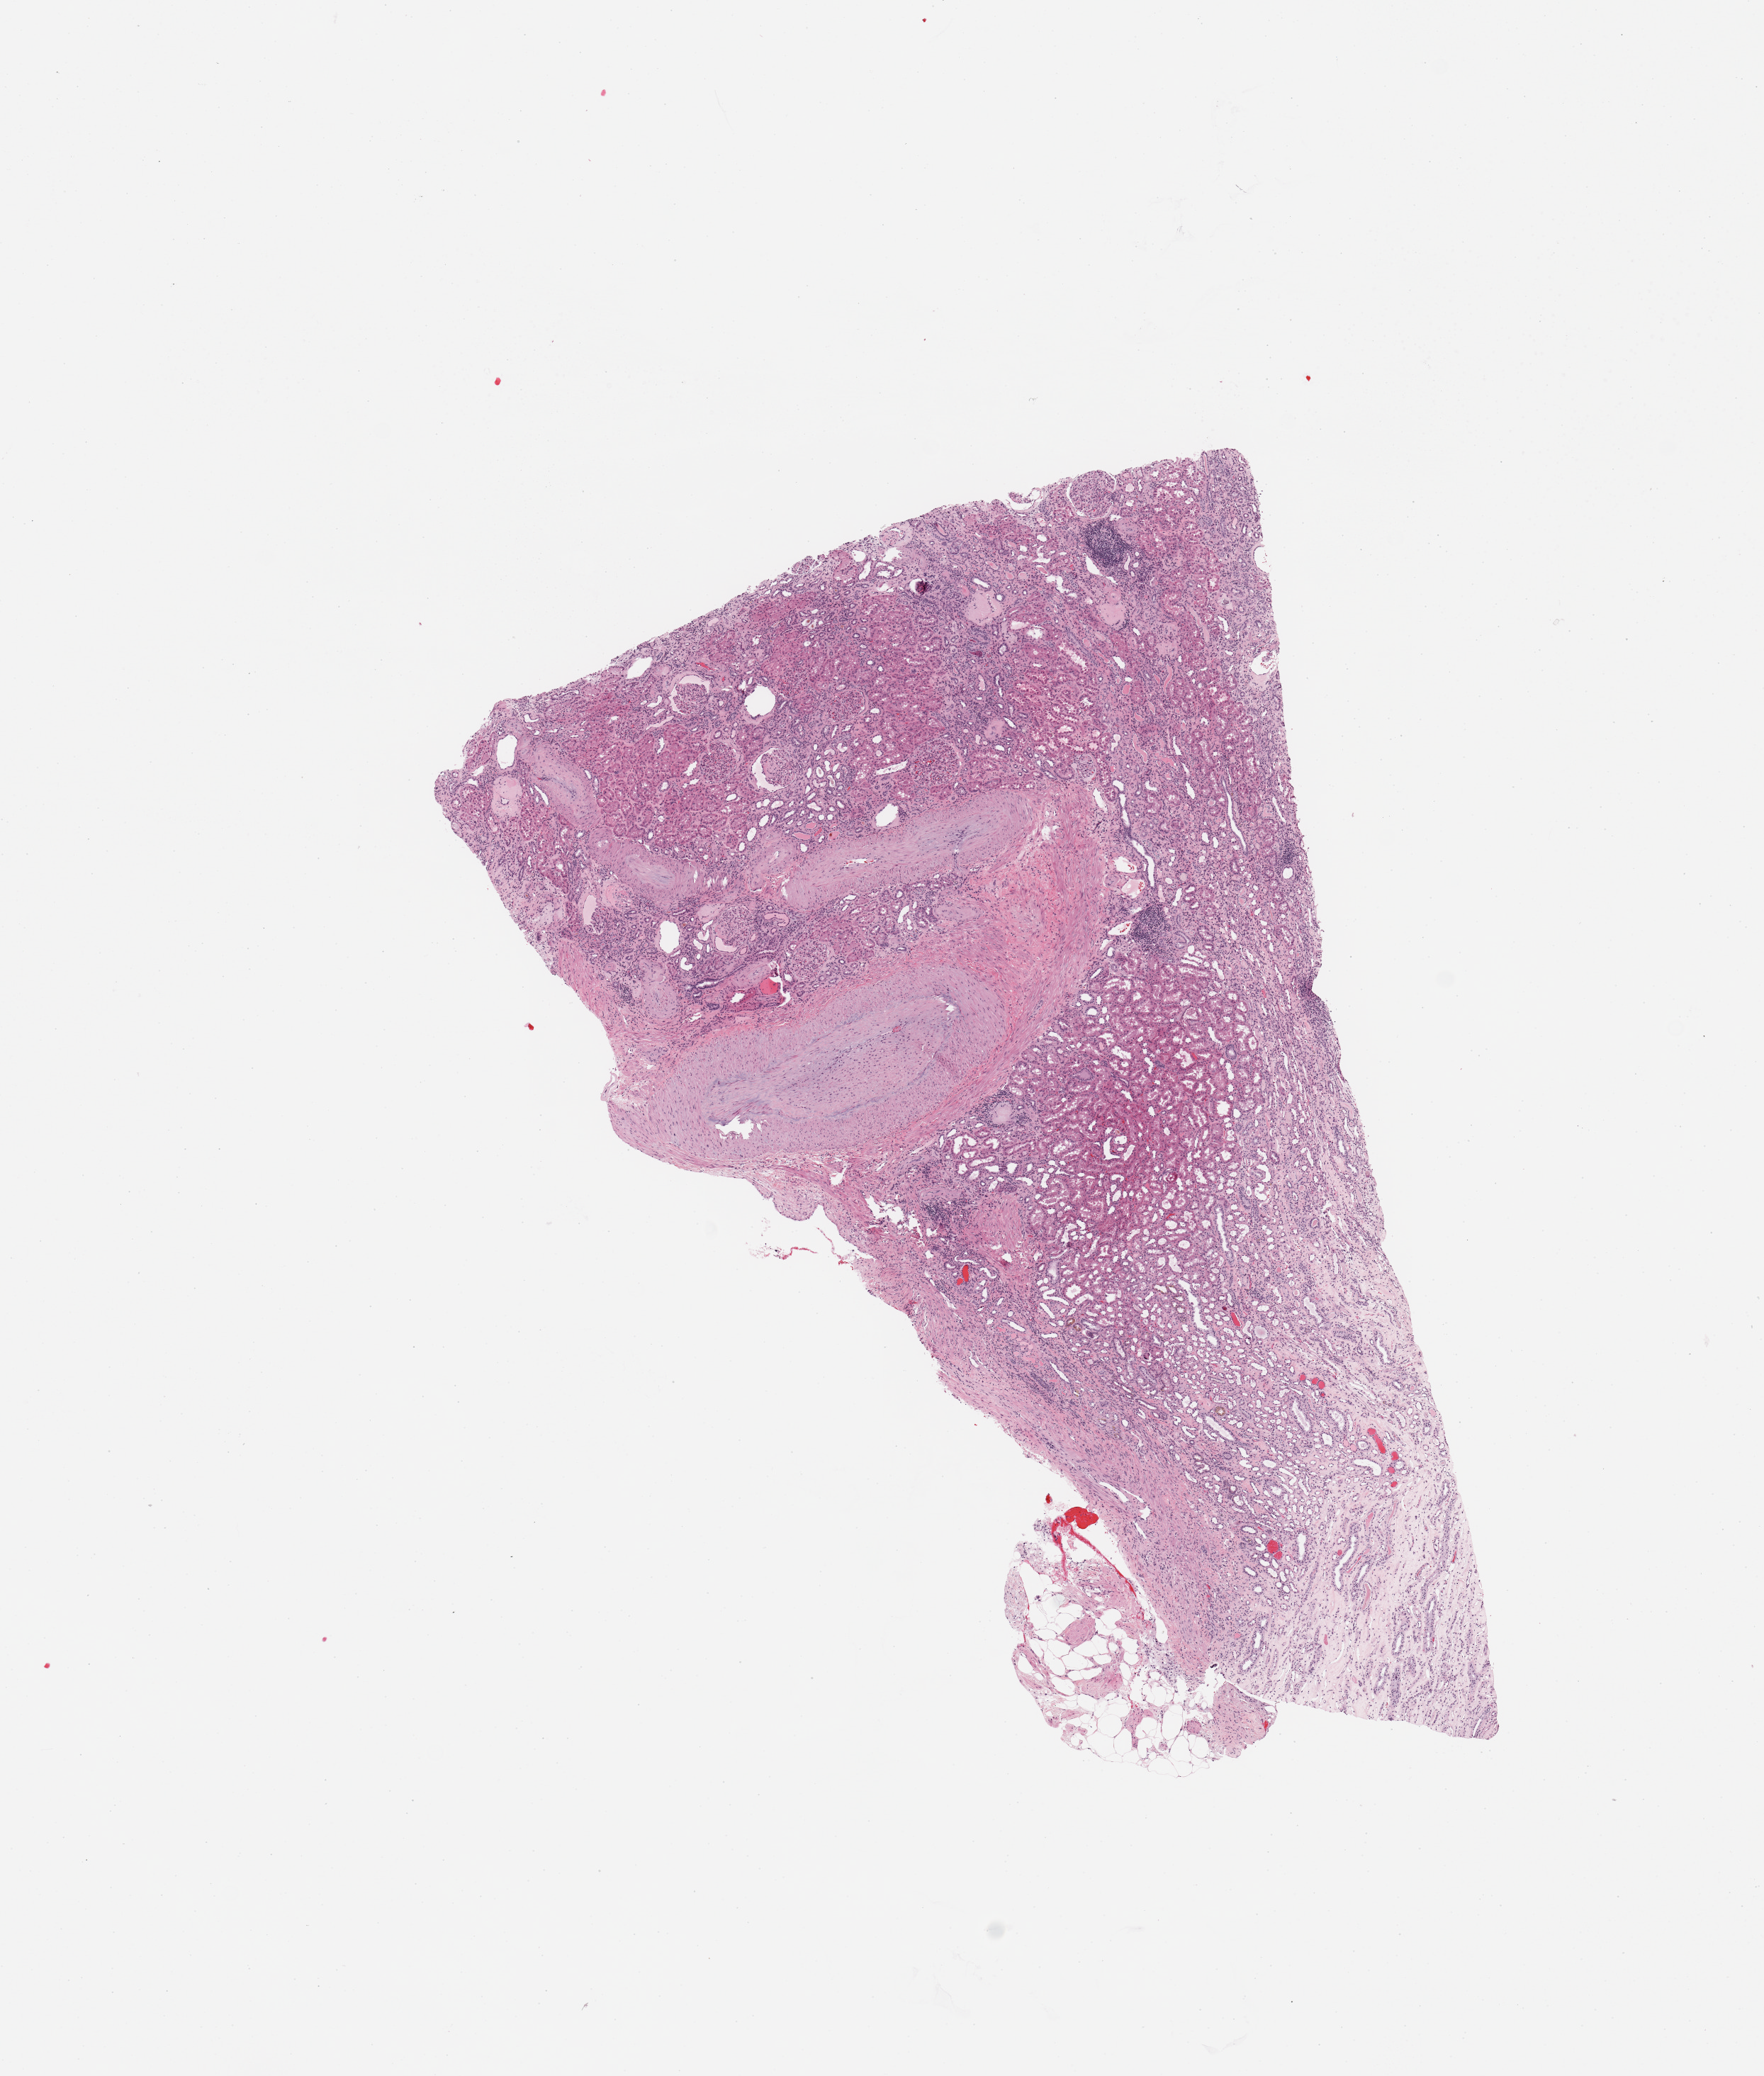
Digitized H&E-stained tissue section (whole slide) — a low-resolution overview of the entire scanned area, about 9.8 x 11.6 mm (from a 20x scan). Normal (non-tumour) tissue sample, sampled site: kidney. 62-year-old male patient.
- this section: normal (non-tumour) tissue from the same patient
- patient diagnosis: Renal cell carcinoma, NOS